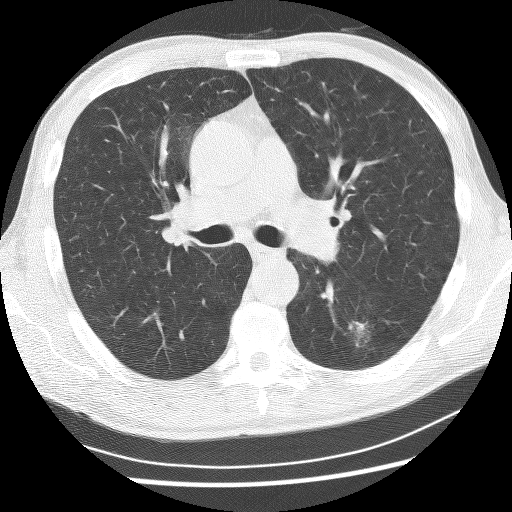
Low-dose screening chest CT, one axial slice; slice 153 of 253 in the series (ordered by position); reconstruction kernel BONE; 120 kVp; lung window (W 1500 / L -600 HU); 2.5 mm slice thickness; 512 × 512 image matrix, field of view 340 × 340 mm.
Annotated regions visible in this slice (expert manual segmentation):
- lesion 1 (tumor, lower lobe of left lung): bounding box (x1, y1, x2, y2) in pixels: (349, 321, 365, 337)